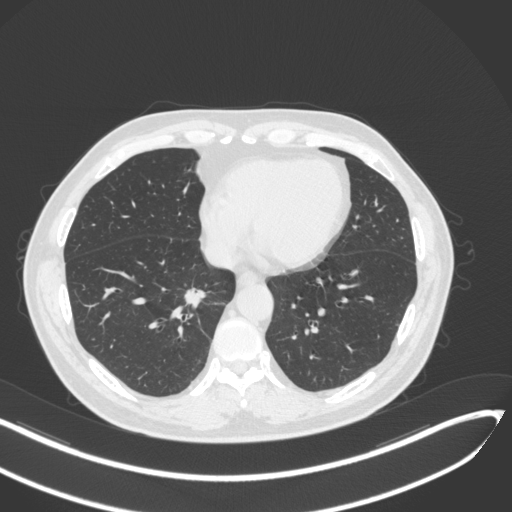
Chest CT, one axial slice; position 129 of 429 along the scan axis; reconstruction kernel B31f; 120 kVp; lung window (W 1500 / L -600 HU); 1 mm slice thickness; 512 × 512 image matrix, field of view 400 × 400 mm. Male patient, age 62 years. From the clinical record (not read from this slice): clinical TNM (as recorded): T1b N0 M0; histopathological grade: G2.
Annotated regions visible in this slice (rectangle marked by the reading radiologist):
- lung tumour (recorded histology: adenocarcinoma): bounding box <180,286,212,311> (left, top, right, bottom; pixels)